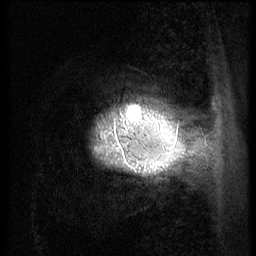
Breast MRI (dynamic contrast-enhanced), one sagittal slice; slice 5 of 56 in the series (ordered by position); 3 images stored at this slice position (order not interpretable as contrast timing); 1.5 T; TE 4.2 ms, TR 9 ms; 256 × 256 image matrix. Patient: female, 49 years. From the clinical record (not read from this slice): setting: breast cancer imaged before/during neoadjuvant chemotherapy; receptor status: HER2-positive.
Annotated regions visible in this slice (semi-automatic segmentation, software-assisted and operator-edited):
- analysis volume of interest (the breast-tissue region the enhancement analysis was run in; not a lesion): box from (x=78, y=79) to (x=152, y=203) px
- tumour enhancement mask (voxels above the 140 % enhancement threshold inside the analysis volume of interest): (x=96, y=116)–(x=137, y=150)